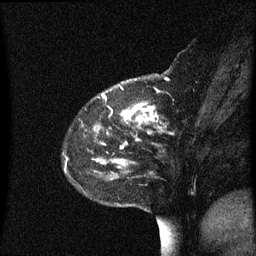
Breast MRI (dynamic contrast-enhanced), one sagittal slice; position 18 of 60 along the scan axis; dynamic contrast-enhanced series, image 2 of 3 at this slice position (ordered by acquisition); 1.5 T; TE 4.2 ms, TR 8.4 ms; 2 mm slice thickness; 256 × 256 image matrix. Female patient, age 48 years. From the clinical record (not read from this slice): setting: breast cancer imaged before/during neoadjuvant chemotherapy; receptor status: HR-positive, HER2-negative.
Structures marked on this image (semi-automatically segmented with operator editing):
- analysis volume of interest (the breast-tissue region the enhancement analysis was run in; not a lesion): bounding box [x1, y1, x2, y2] px = [82, 78, 195, 221]
- tumour enhancement mask (voxels above the 70 % enhancement threshold inside the analysis volume of interest): [102, 95, 159, 163]